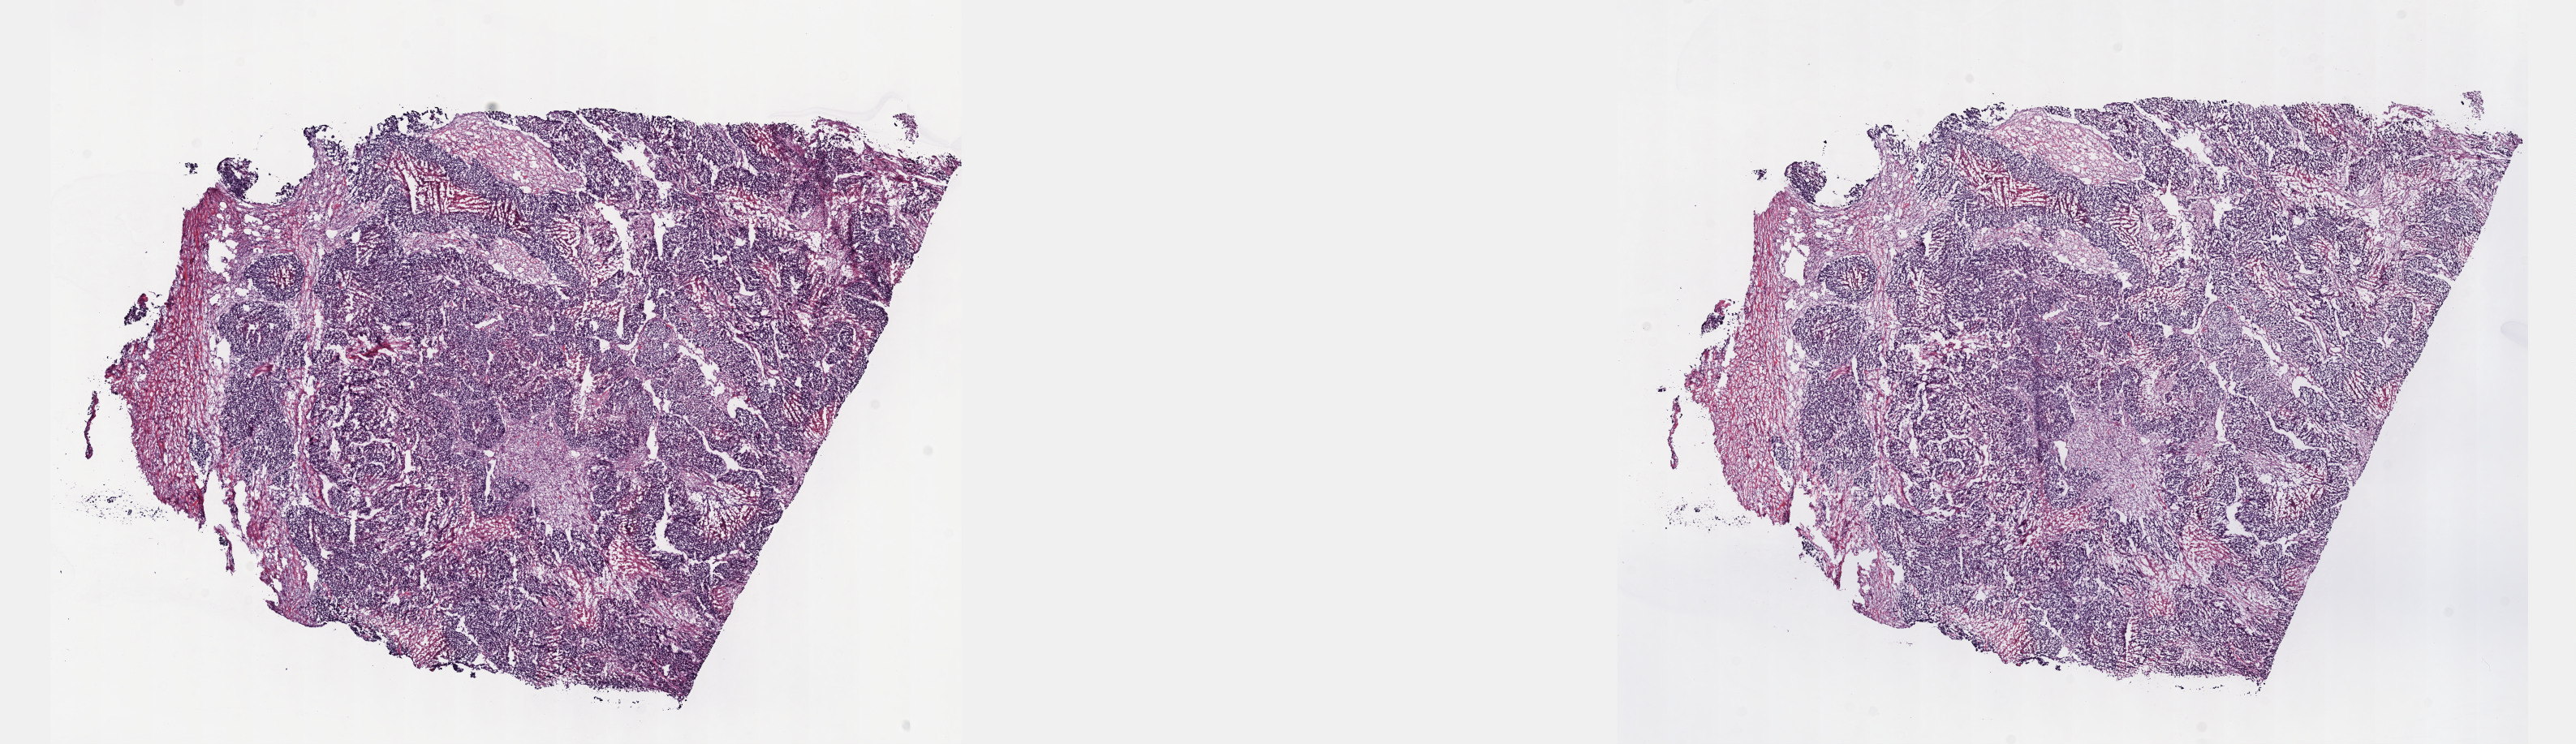
Hematoxylin and eosin (H&E) stained whole-slide image — whole scanned area (about 25.7 x 7.4 mm, acquisition: 40x scan) shown as a low-resolution overview; frozen section; sample: primary tumour, bladder. Patient: male, age at initial diagnosis 54 years. Histologic grade: high grade. Composition of this section per pathologist review: tumour cells 100%, tumour nuclei 65%, normal cells 0%, stromal cells 0%, necrosis 0%. Inflammatory infiltration, as recorded: lymphocyte infiltration 3%, monocyte infiltration 0%, neutrophil infiltration 0%.
* lymph nodes positive (case pathology): 0 of 141 examined
* AJCC pathologic stage: III (5th edition)
* pathologic diagnosis: Transitional cell carcinoma